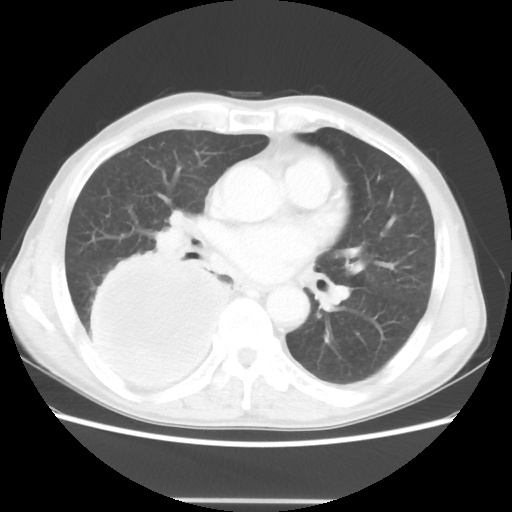
Chest CT, one axial slice. Slice 23 of 48 in the series (ordered by position). 100 kVp. Lung window (W 1500 / L -600 HU). 5 mm slice thickness. 512 × 512 image matrix. Male patient, age 66 years. Case-level facts recorded for this patient, not image findings: clinical TNM (as recorded): T4 N1 M1; histopathological grade: G3.
Outlined on this slice (bounding box drawn by a radiologist):
- lung tumour (recorded histology: small cell carcinoma): bounding box (x1, y1, x2, y2) in pixels: (84, 253, 230, 398)